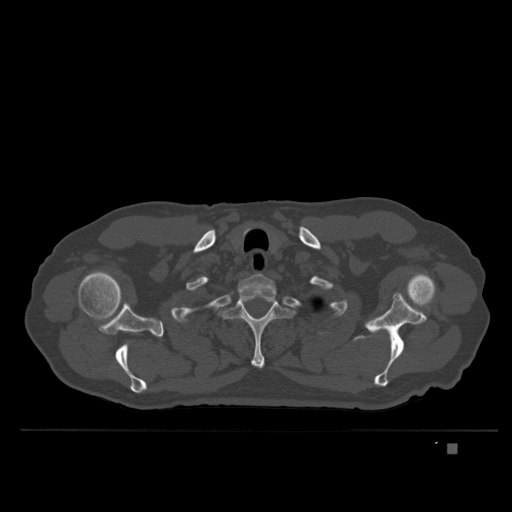
CT including the spine, one axial slice. Slice 315 of 435 in the series (ordered by position). Bone window (W 1800 / L 400 HU). 1.5 mm slice thickness. 512 × 512 image matrix, field of view 434 × 434 mm. Male patient, age 73 years. Case-level facts recorded for this patient, not image findings: primary cancer: skin.
Annotated regions visible in this slice (semi-automatic segmentation, software-assisted and operator-edited):
- T1 vertebra: bounding box [x1, y1, x2, y2] px = [237, 273, 276, 292]
- T2 vertebra: [221, 295, 293, 368]